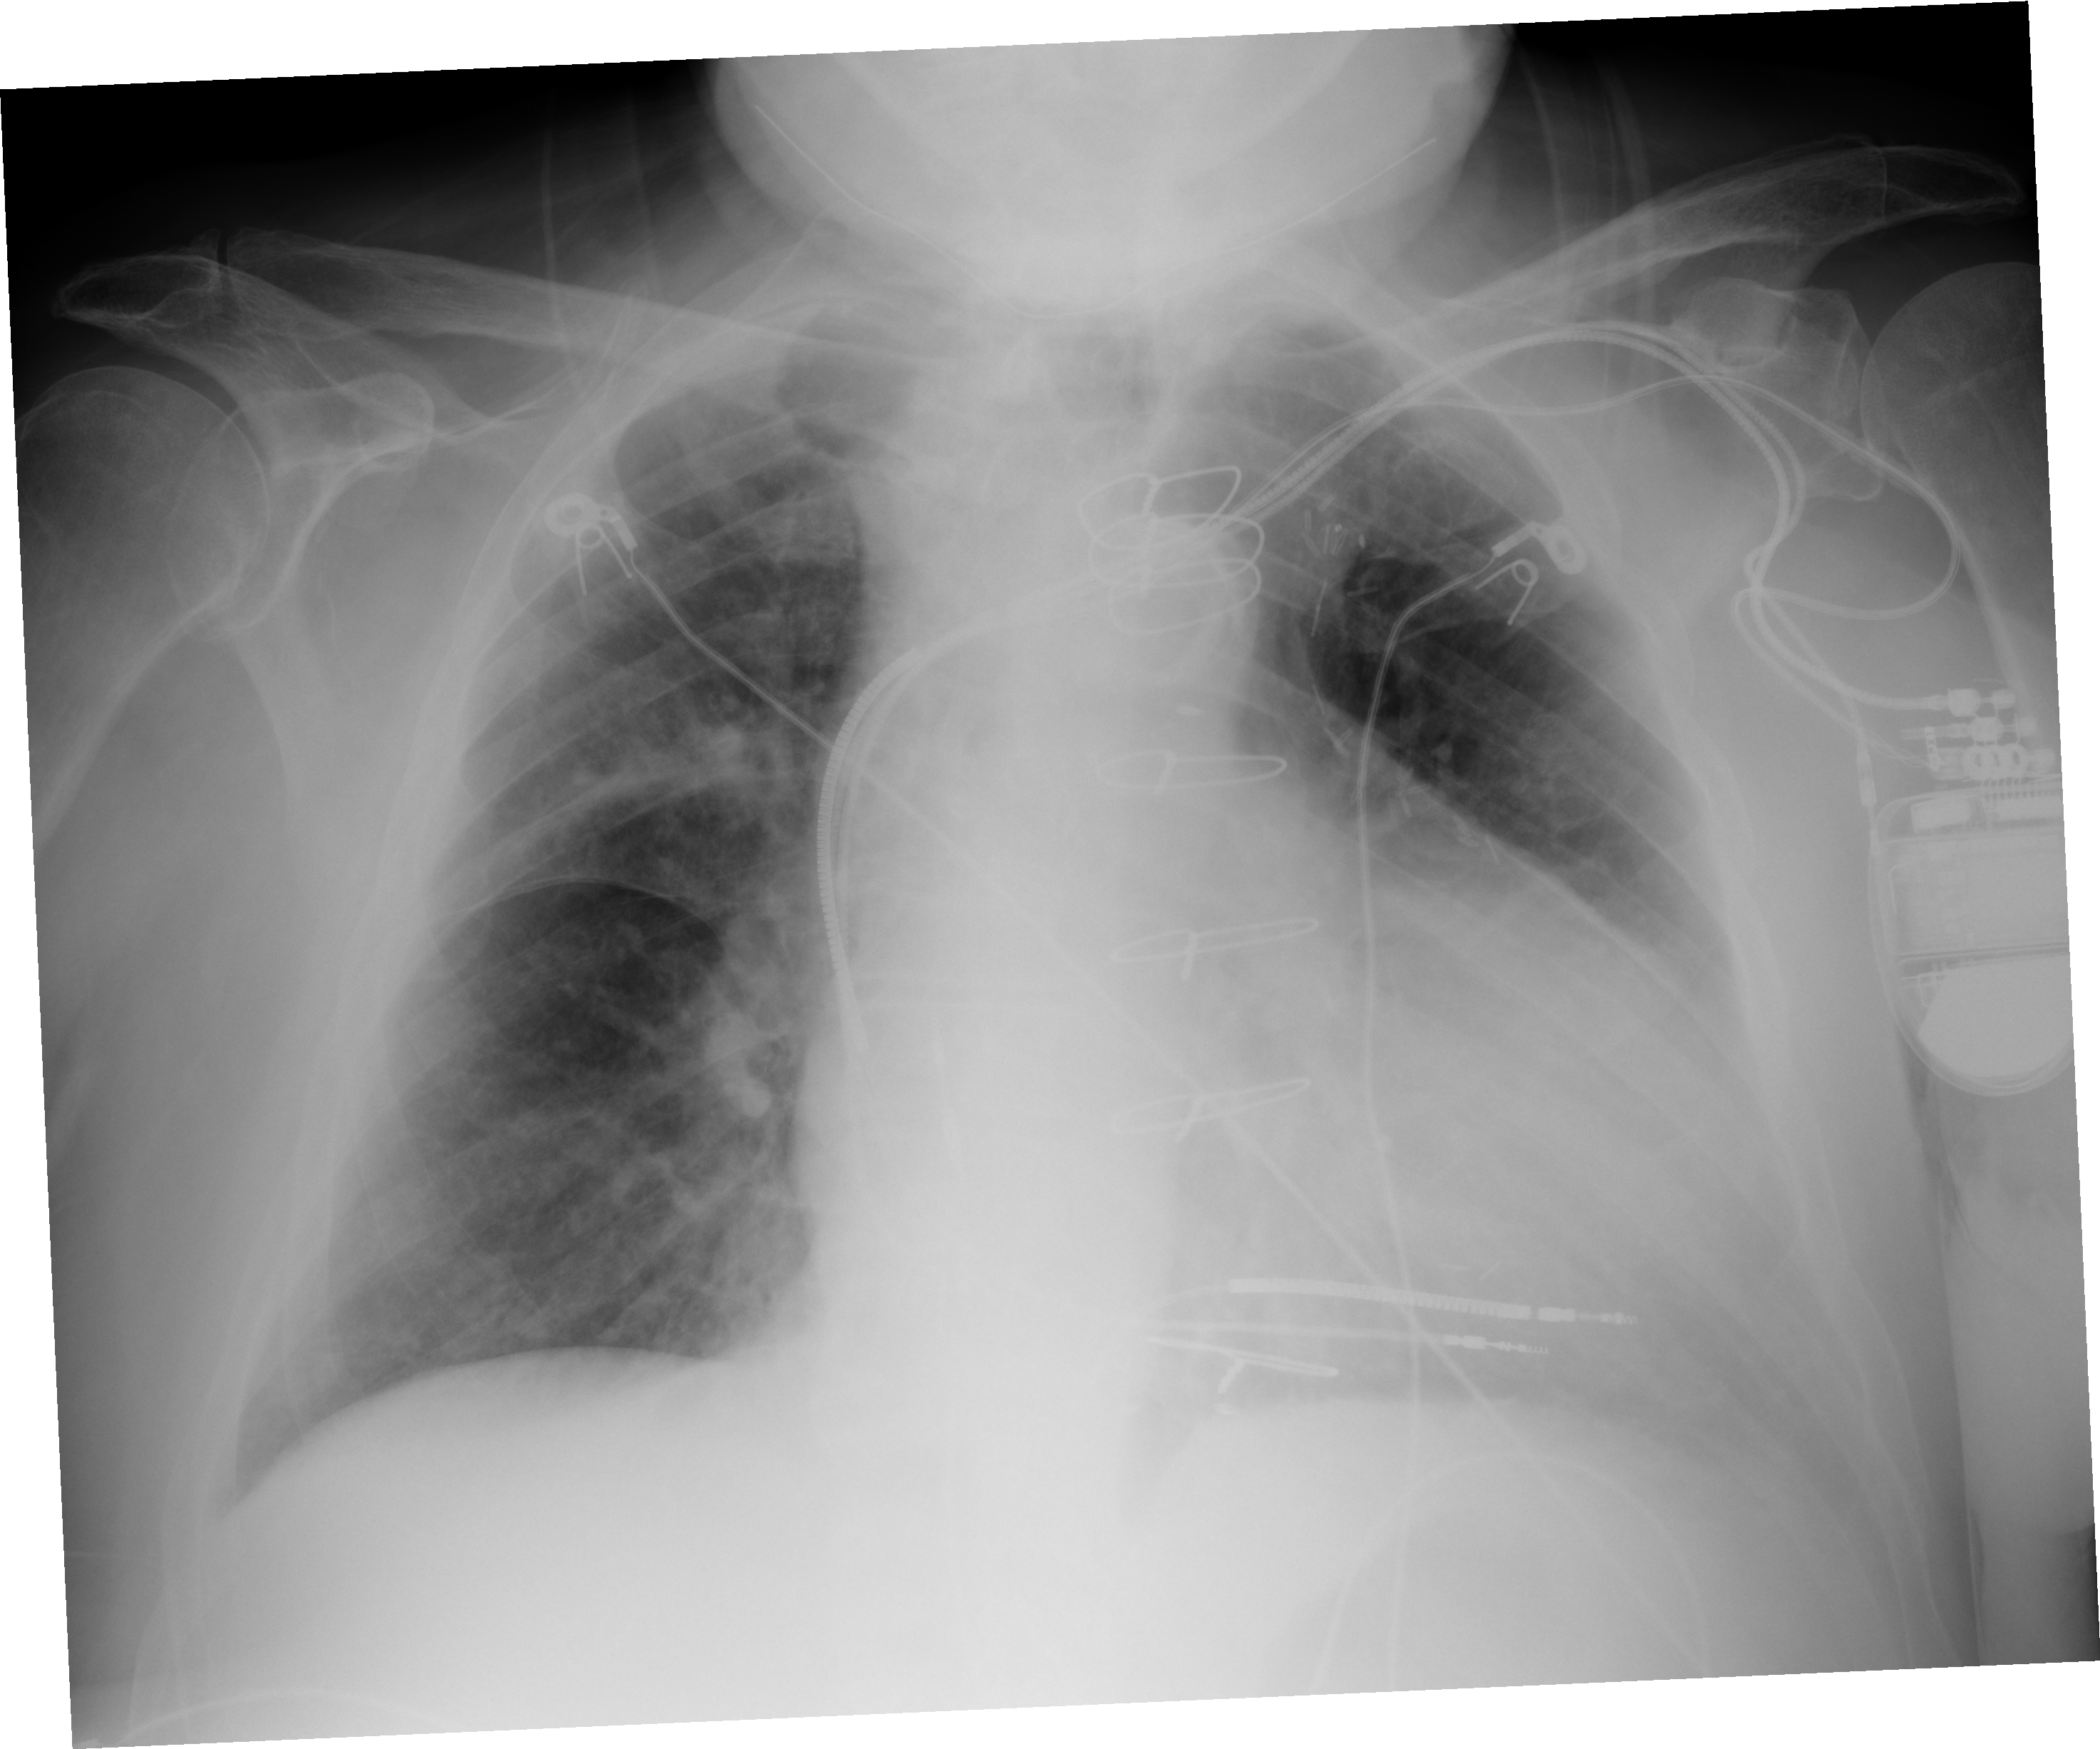
Portable chest radiograph, AP projection. Male patient, age 87 years; imaged 0 days after the COVID-19 diagnosis.
Key findings recorded by the radiologist: Haziness of the left cardiac border.